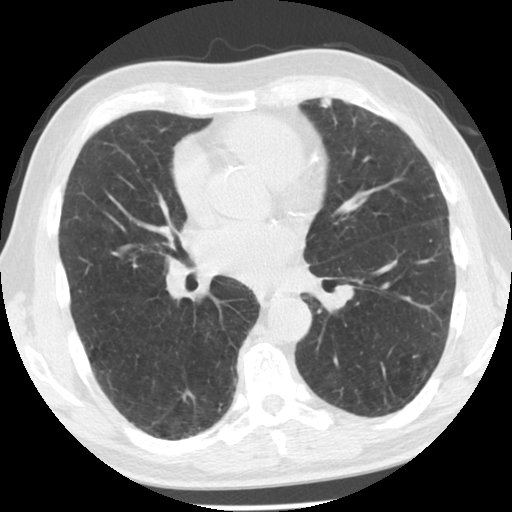
Low-dose screening chest CT, one axial slice. Position 63 of 129 along the scan axis. Reconstruction kernel STANDARD. 140 kVp. Lung window (W 1500 / L -600 HU). 512 × 512 image matrix, field of view 330 × 330 mm.
Structures marked on this image (outlined manually by an expert reader):
- lesion 1 (tumor, upper lobe of left lung): box from (x=320, y=97) to (x=332, y=108) px